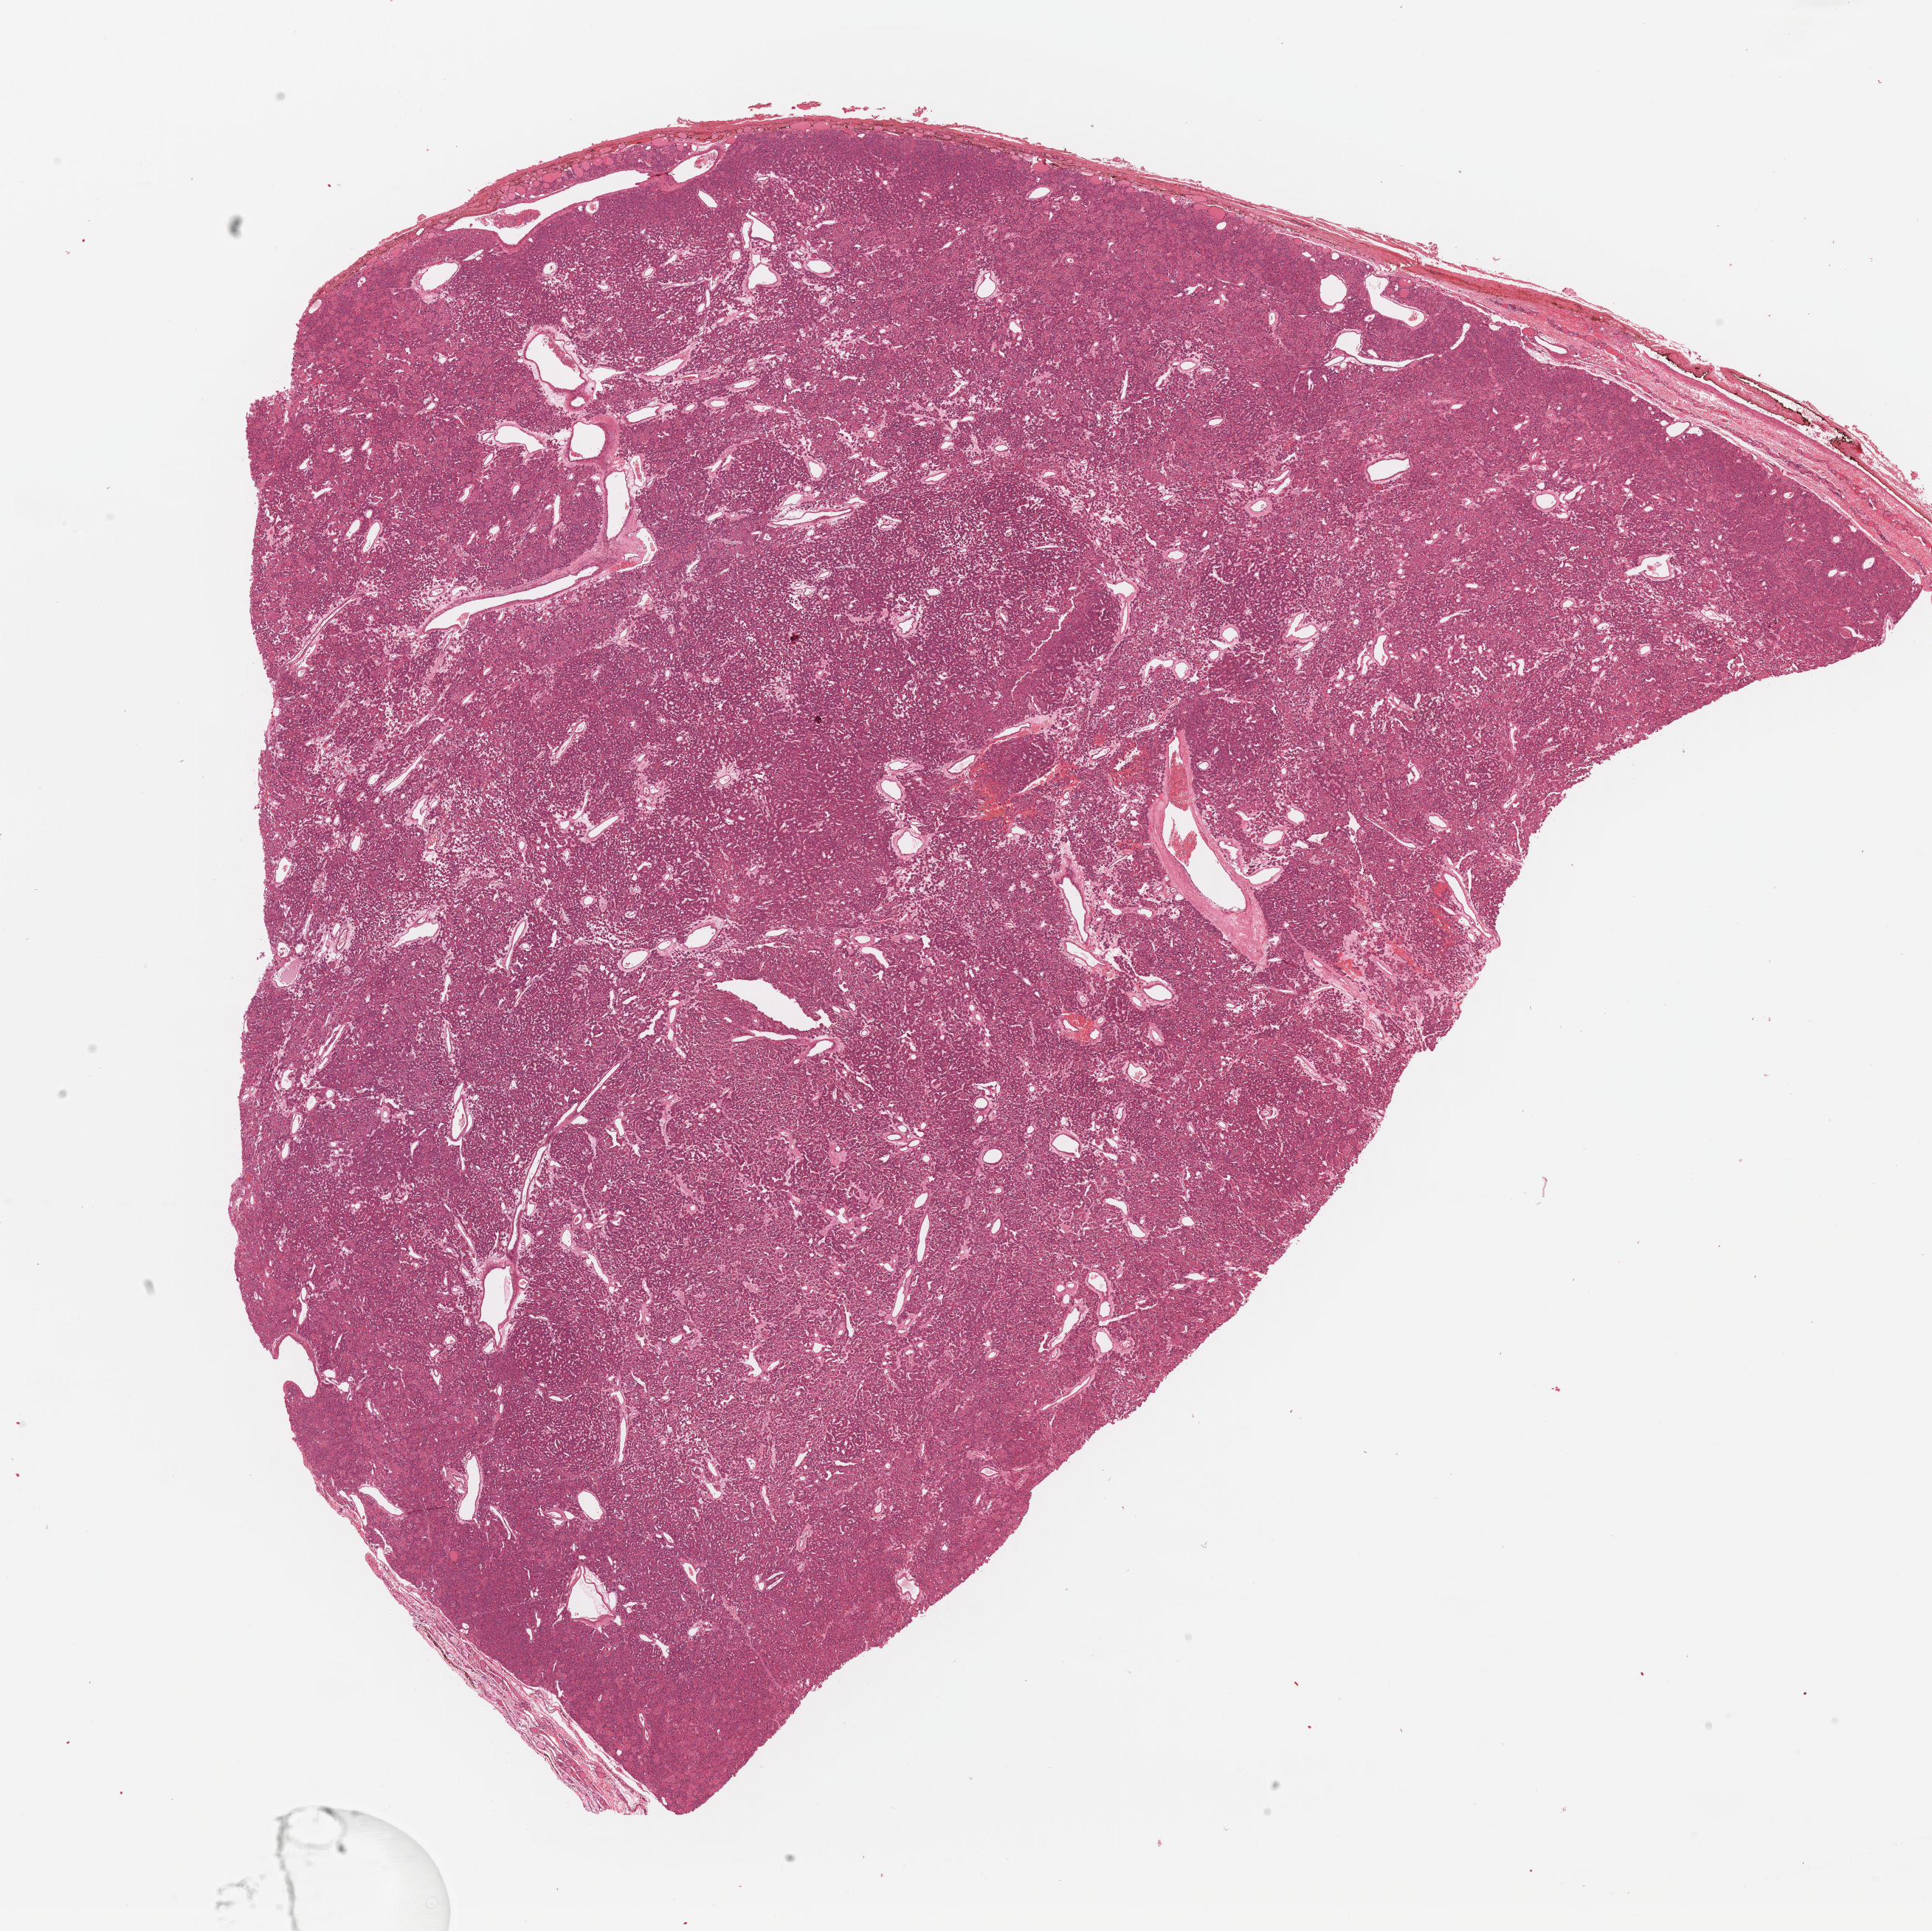
Whole-slide histology image, Hematoxylin and eosin (H&E) stained, low-resolution overview of the scanned area, about 20.7 x 20.6 mm (from a 40x scan), formalin-fixed paraffin-embedded (FFPE) diagnostic section, sample: primary tumour, thyroid. Female patient; age at initial diagnosis 71 years.
TNM: T3 N0 MX. AJCC pathologic stage: III (6th edition). Diagnosis: Papillary carcinoma, follicular variant (thyroid gland). Lymph nodes positive (case pathology): 0 of 1 examined.